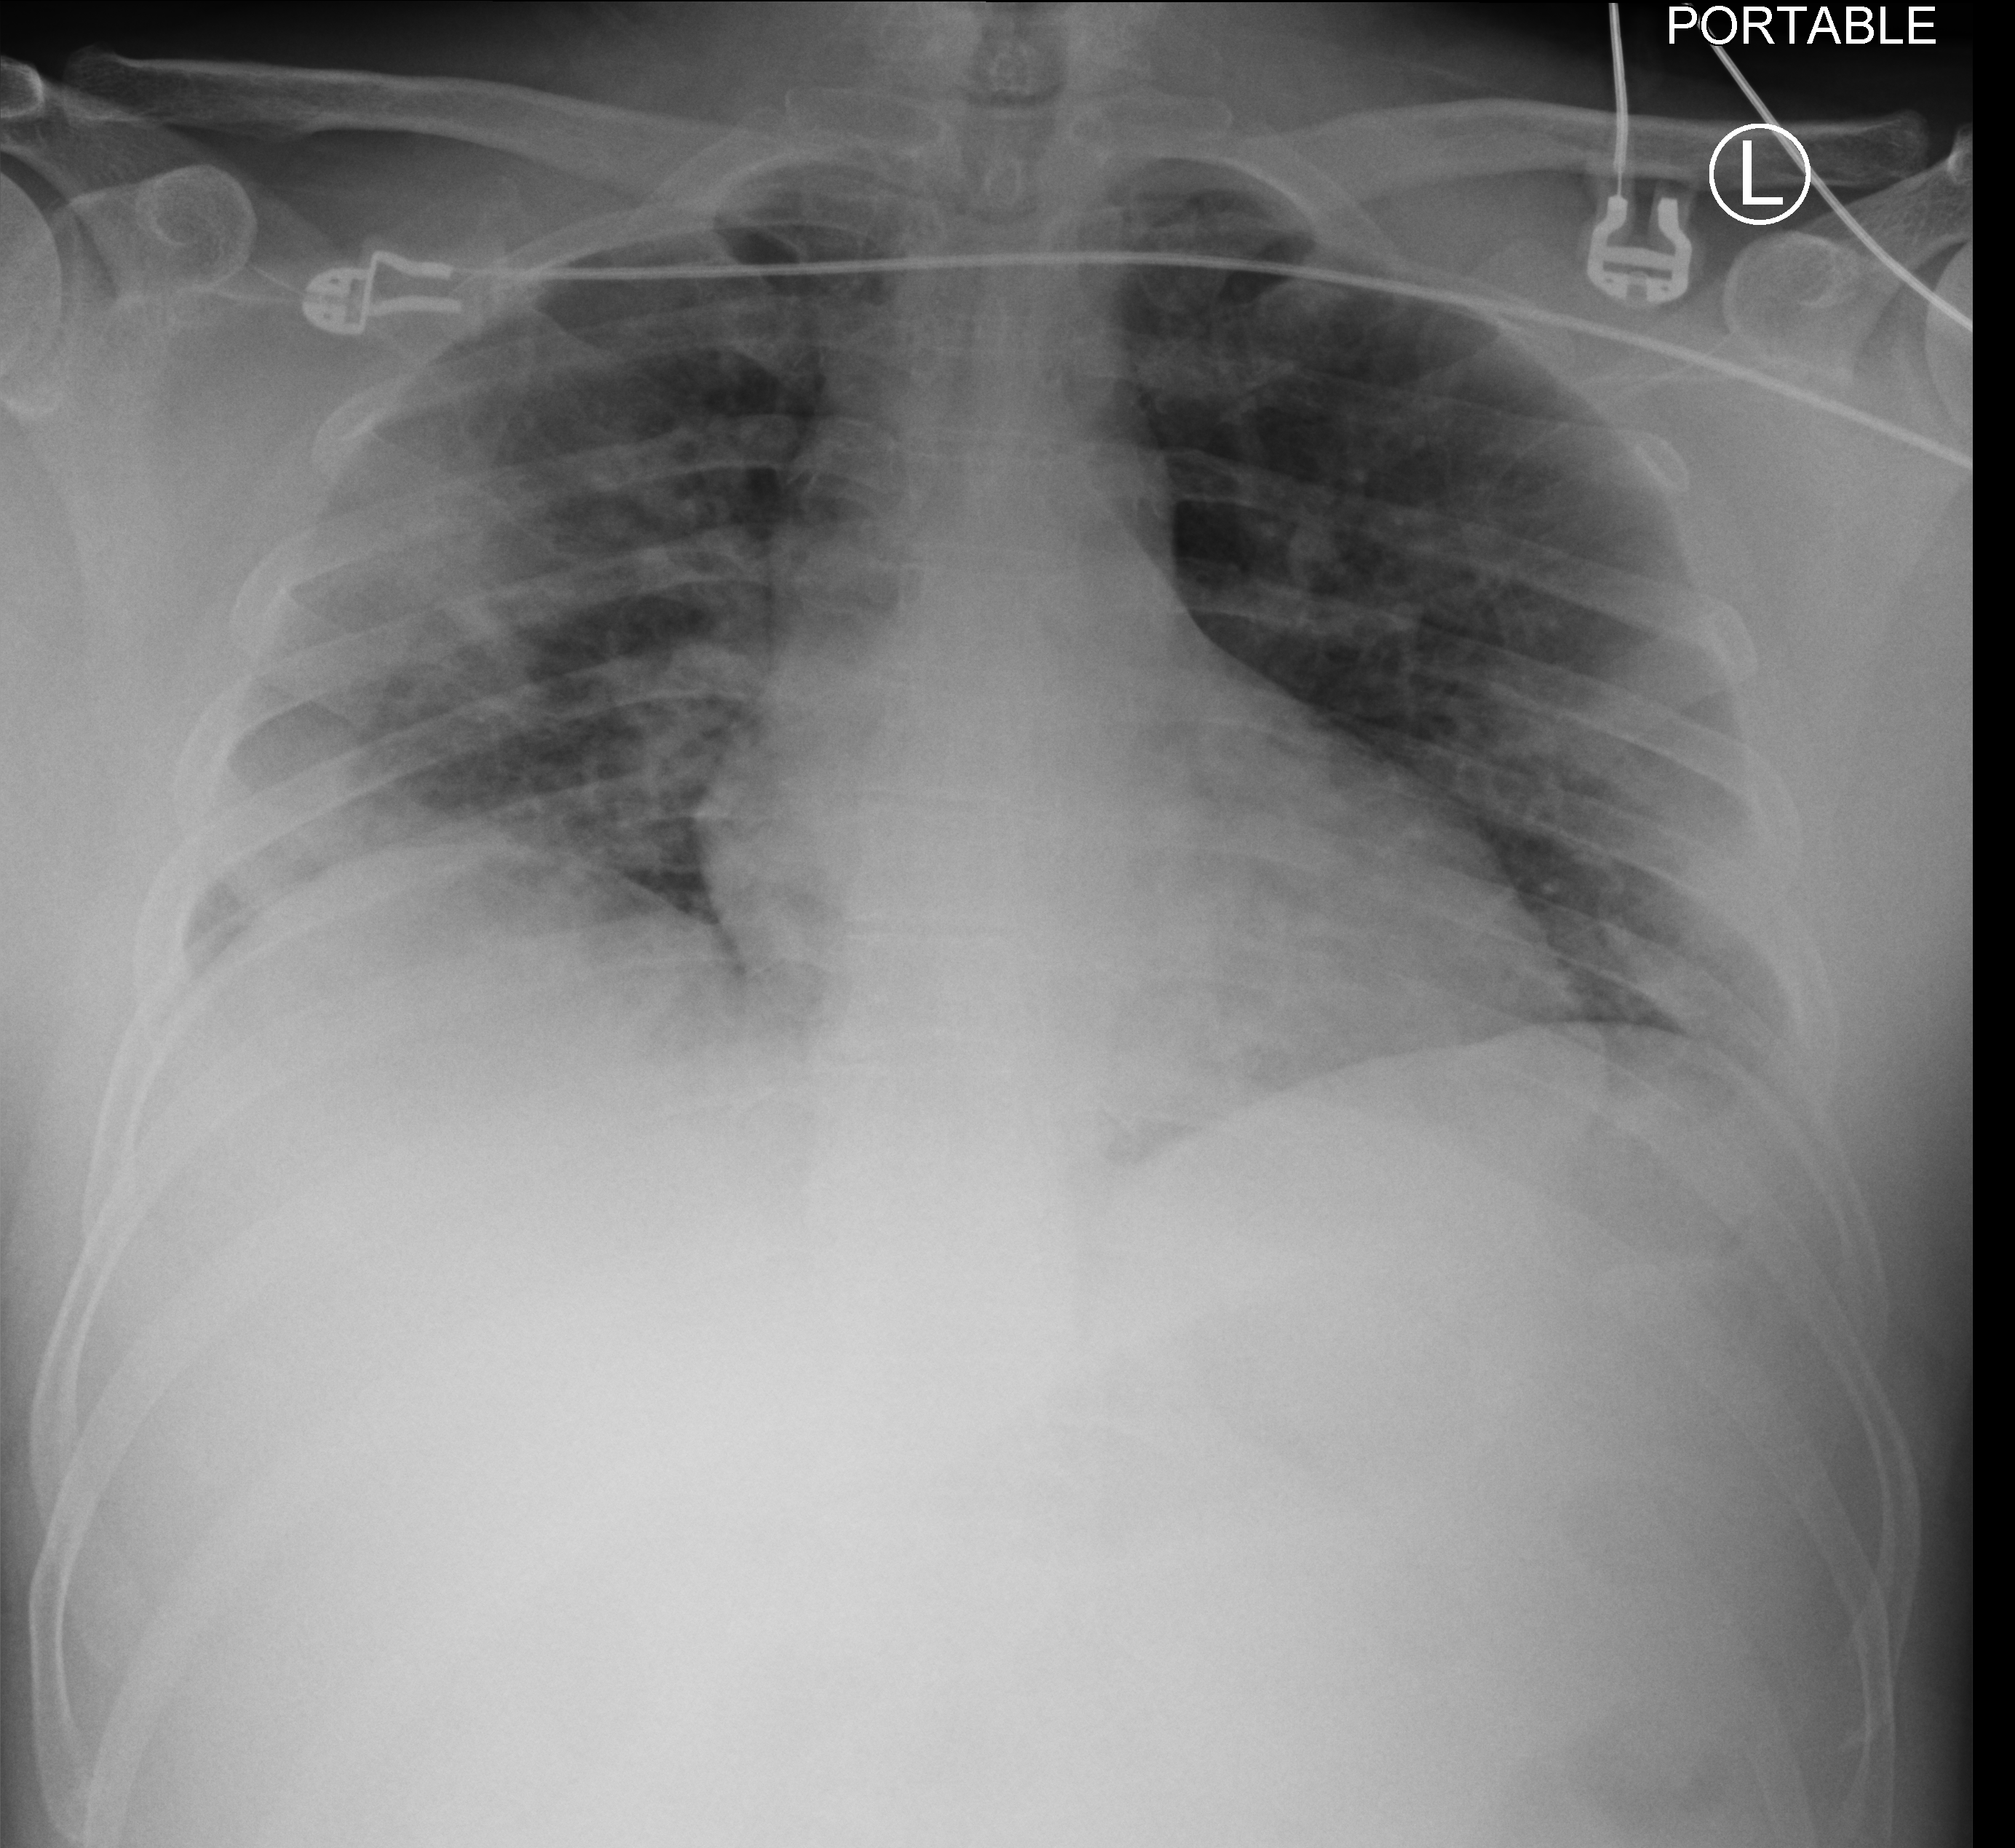
Chest X-ray (portable), anteroposterior (AP) projection. Patient hospitalised with COVID-19; male, aged 18–59 years.
From the hospital-stay record, not from the radiograph (when in the stay this image was taken is not recorded): mechanically ventilated during this hospital stay: no.